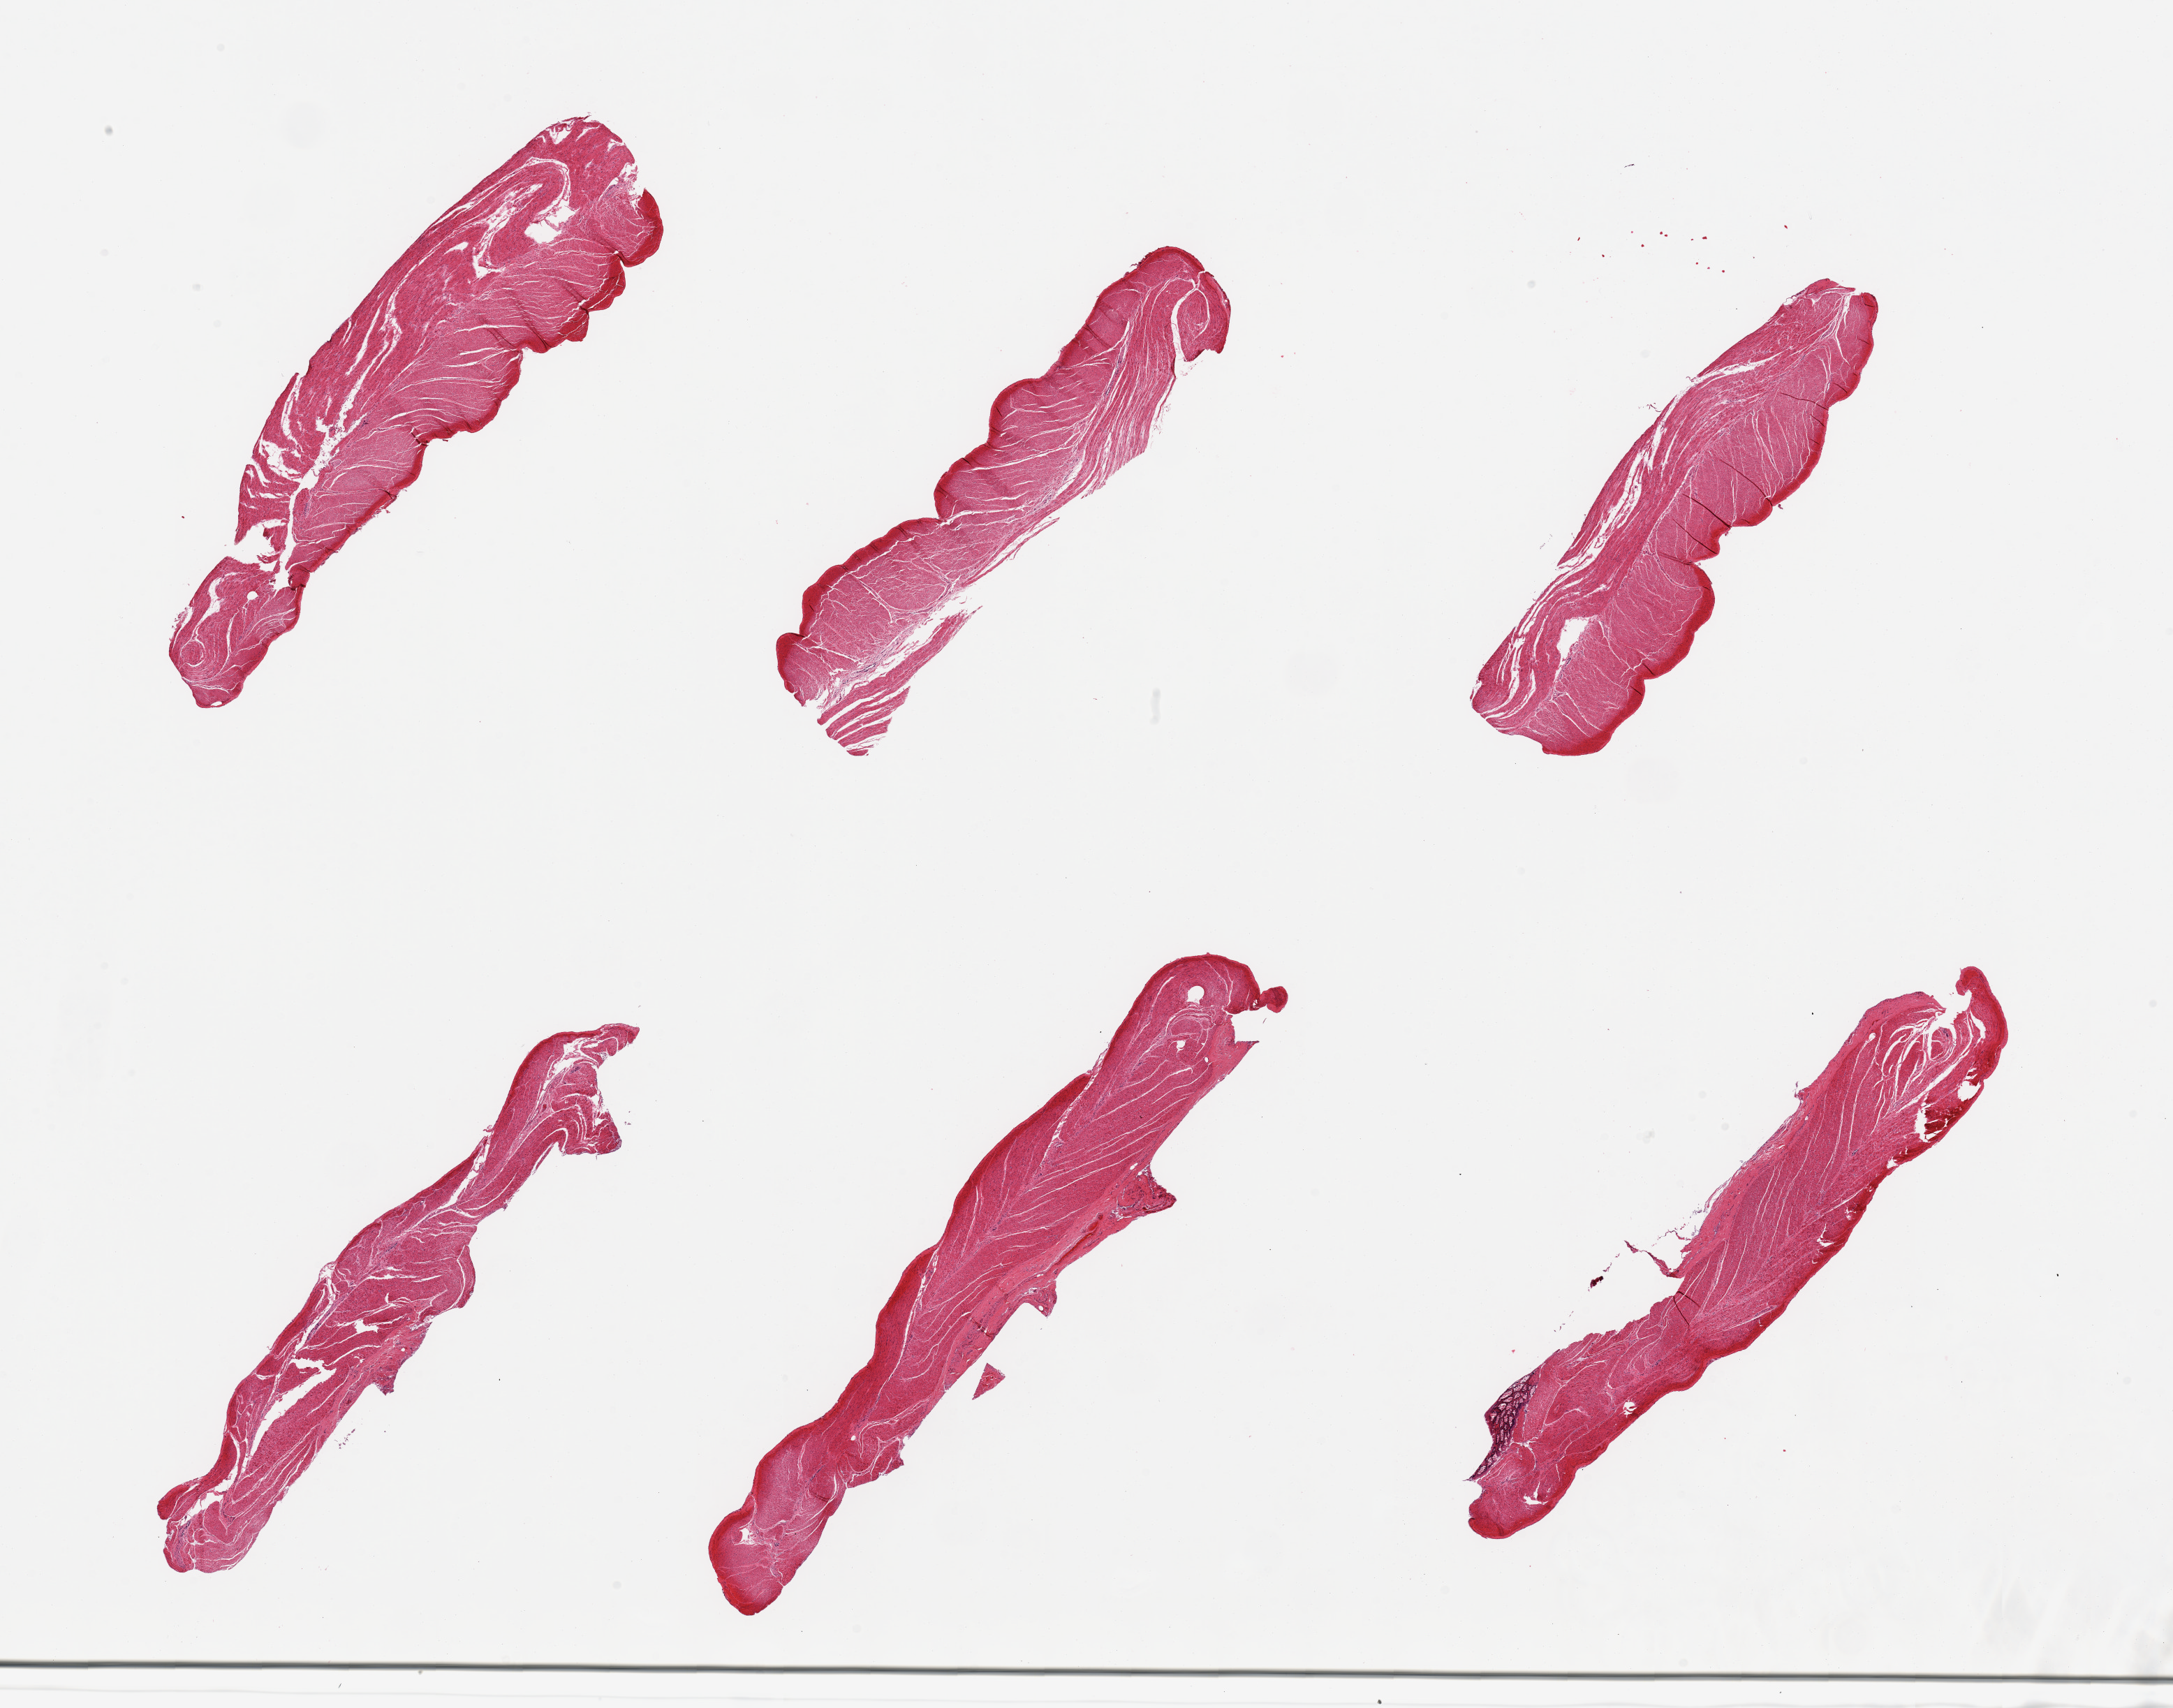
Digitized haematoxylin and eosin-stained section, low-resolution overview of the scanned area, about 24.6 x 19.3 mm, PAXgene-fixed, paraffin-embedded tissue, target tissue: sigmoid colon, donor tissue sample. Male donor.
• pathologist's review note for this sample: 6 pieces, all target muscularis